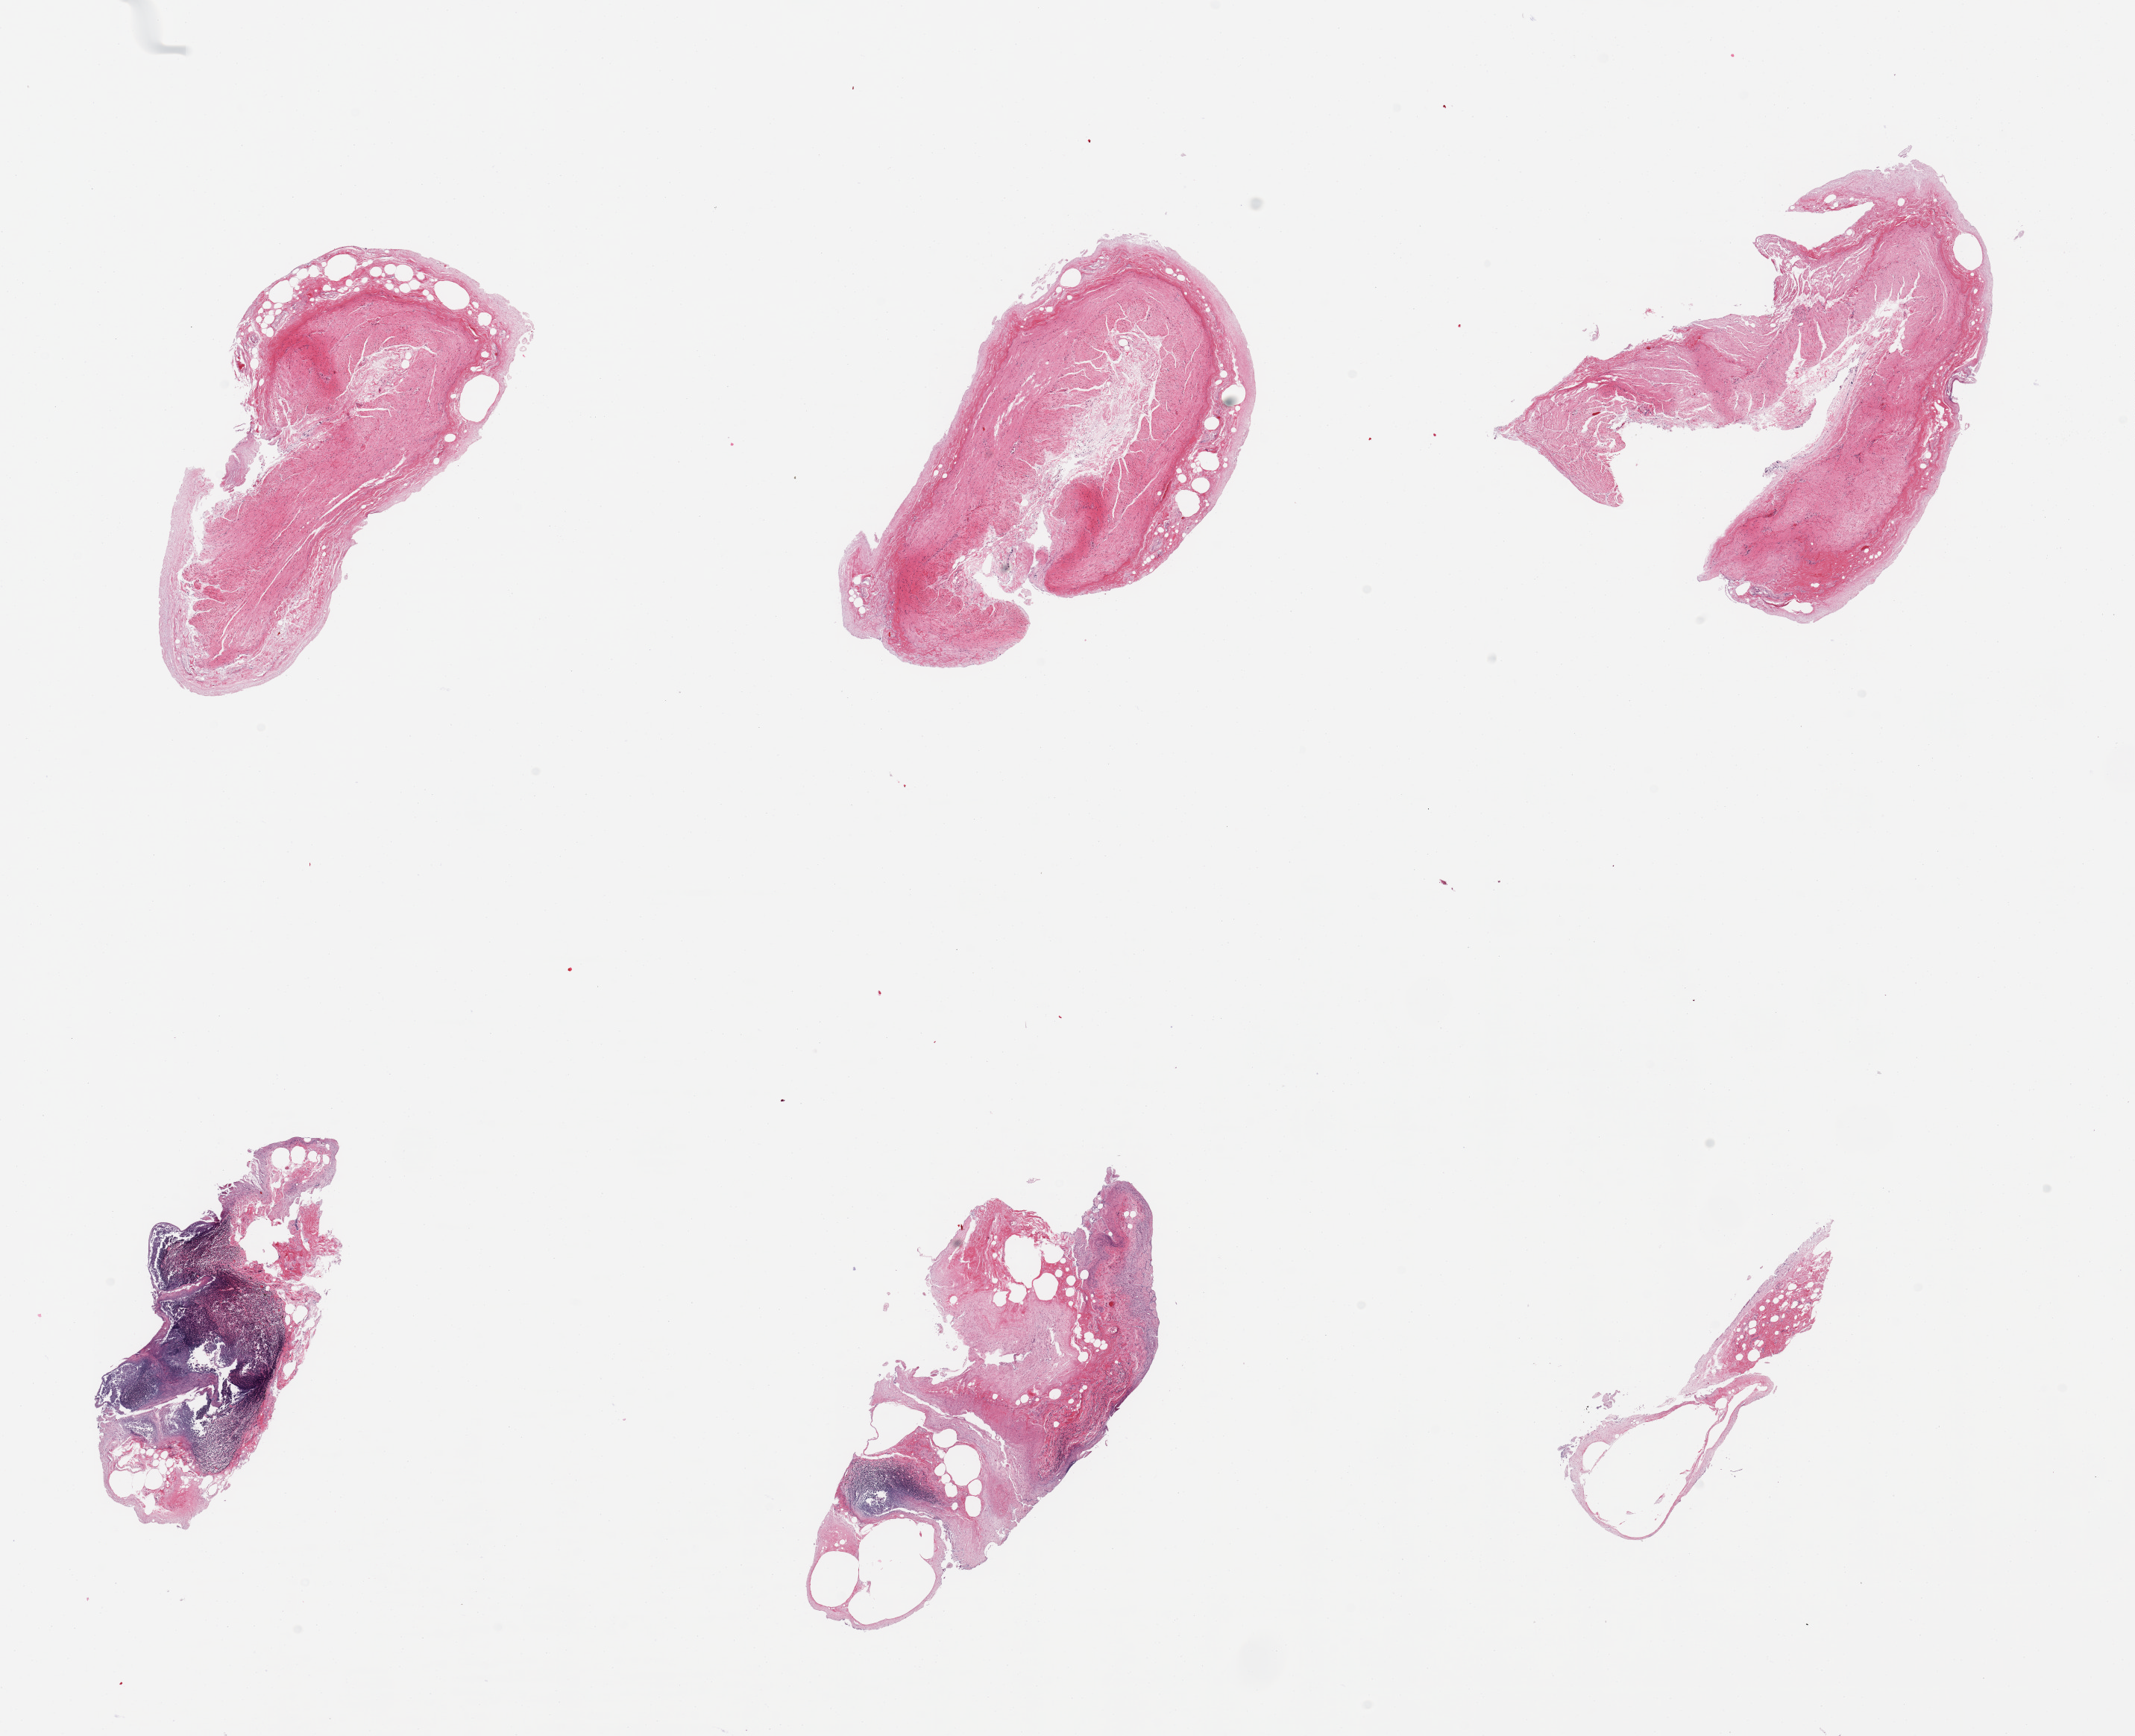
Digitized haematoxylin and eosin-stained section, brightfield — whole scanned area (about 22.6 x 18.4 mm) shown as a low-resolution overview; PAXgene-fixed paraffin-embedded (PFPE) section; sampled site (target tissue): ileum; tissue donor sample. Male donor.
Review note (as recorded): 6 pieces; full thickness (muscularis not target), autolyzed.